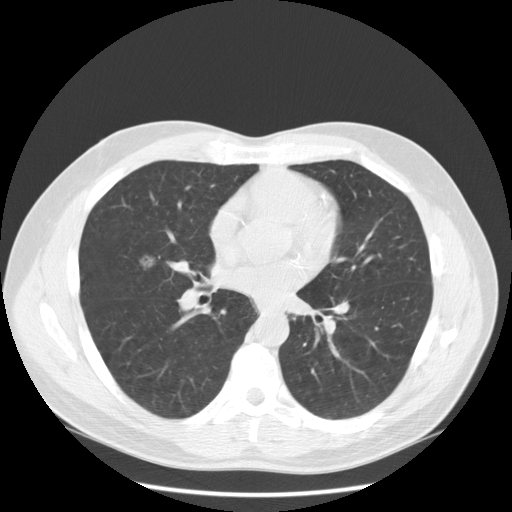
Low-dose screening chest CT, one axial slice; slice 109 of 234 in the series (ordered by position); lung window (W 1500 / L -600 HU); 2.5 mm slice thickness; 512 × 512 image matrix, field of view 385 × 385 mm.
Annotated regions visible in this slice (manually delineated by an expert):
- lesion 1 (tumor, middle lobe of right lung): bounding box (x1, y1, x2, y2) in pixels: (140, 255, 156, 268)